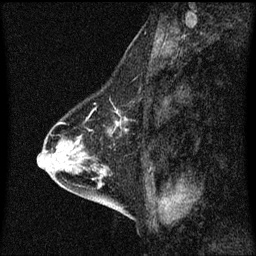
Breast MRI (dynamic contrast-enhanced), one sagittal slice; slice 25 of 60 in the series (ordered by position); dynamic contrast-enhanced series, image 2 of 3 at this slice position (ordered by acquisition); 1.5 T; TE 4.2 ms, TR 8.4 ms; 256 × 256 image matrix. Female patient, age 58 years.
Annotated regions visible in this slice (semi-automatically segmented with operator editing):
- analysis volume of interest (the breast-tissue region the enhancement analysis was run in; not a lesion): bounding box (x1, y1, x2, y2) in pixels: (87, 94, 129, 141)
- tumour enhancement mask (voxels above the 70 % enhancement threshold inside the analysis volume of interest): (91, 110, 127, 133)